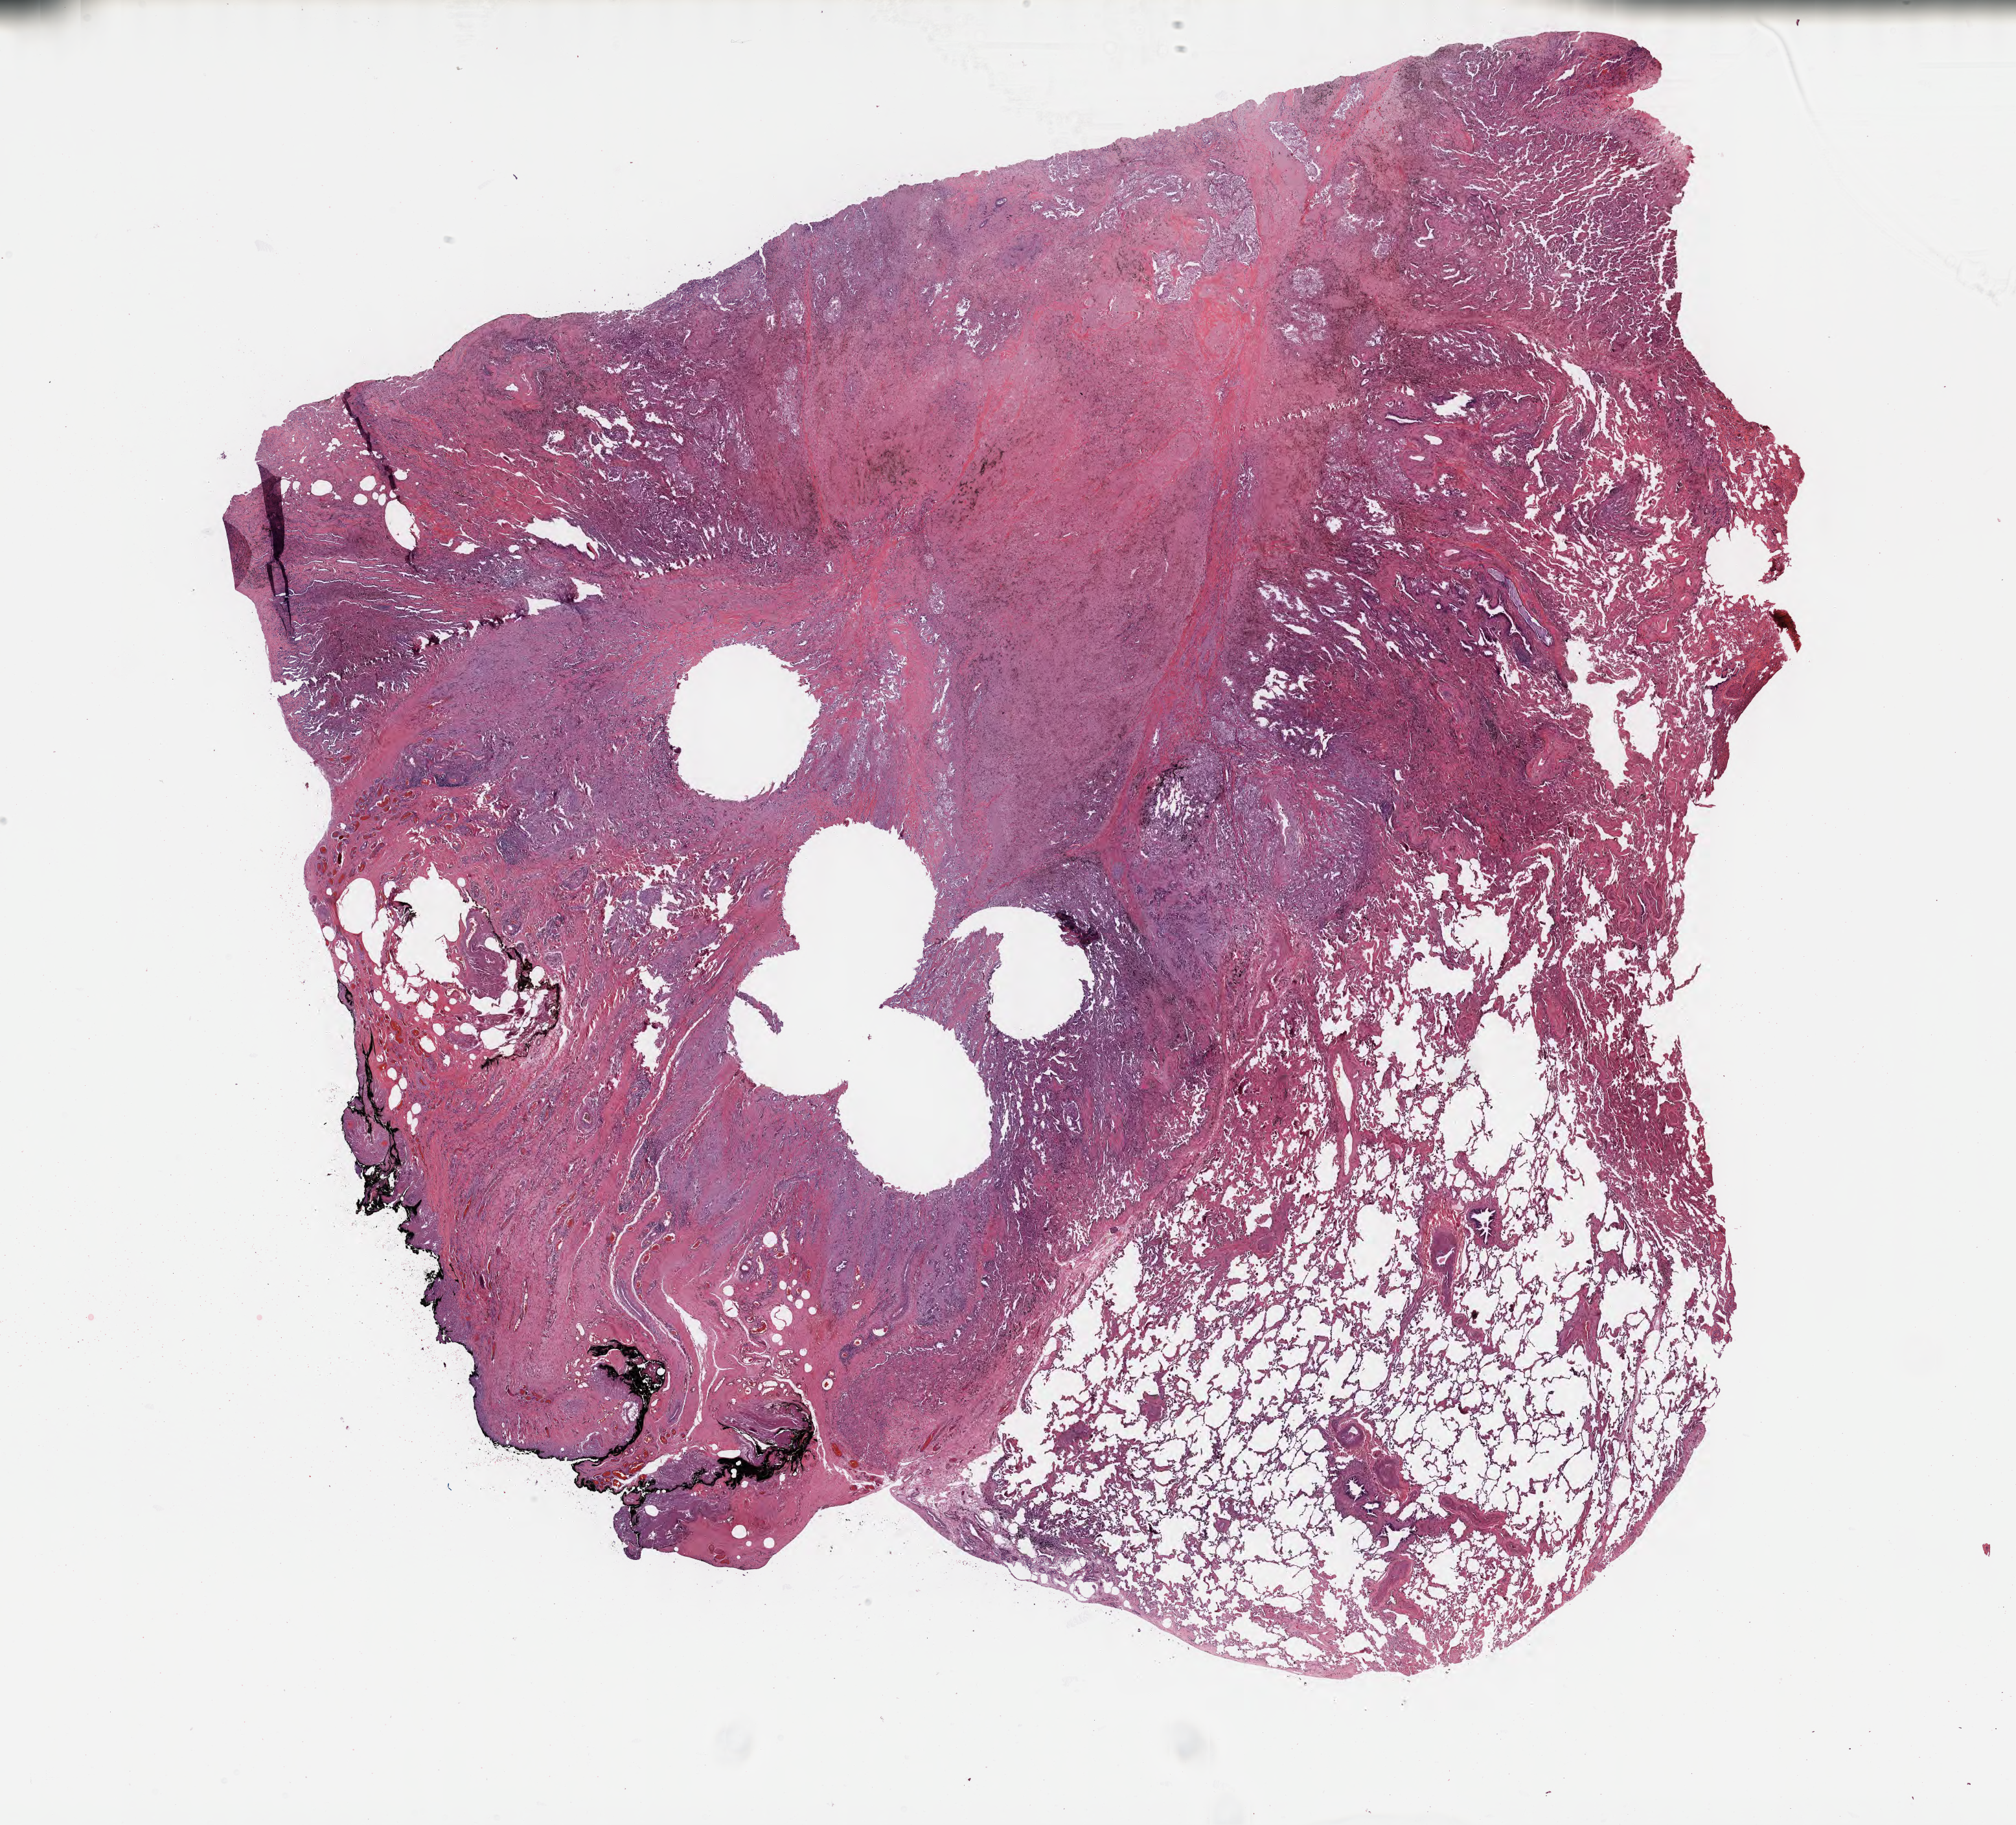
Haematoxylin and eosin whole-slide image, shown as a low-resolution overview of the whole scanned area (about 25.1 x 22.8 mm), tumor tissue. Male patient.
Histologic diagnosis: Adenocarcinoma, NOS.